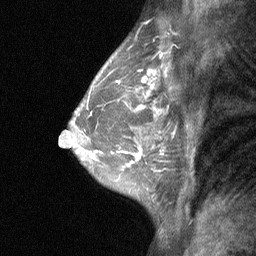
Breast MRI (dynamic contrast-enhanced), one sagittal slice; slice 43 of 64 in the series (ordered by position); dynamic contrast-enhanced study with each time point stored as its own series, time point 2 of 3 at this slice position (early post-contrast, ordered by acquisition time); 1.5 T; TE 4.8 ms, TR 27 ms; 256 × 256 image matrix, field of view 180 × 180 mm. Patient: female, 47 years. Case-level facts recorded for this patient, not image findings: setting: breast cancer imaged before/during neoadjuvant chemotherapy; receptor status: HR-positive, HER2-negative.
Outlined on this slice (semi-automatic segmentation, software-assisted and operator-edited):
- analysis volume of interest (the breast-tissue region the enhancement analysis was run in; not a lesion): bounding box <104,138,164,198> (left, top, right, bottom; pixels)
- tumour enhancement mask (voxels above the 90 % enhancement threshold inside the analysis volume of interest): <125,149,142,167>